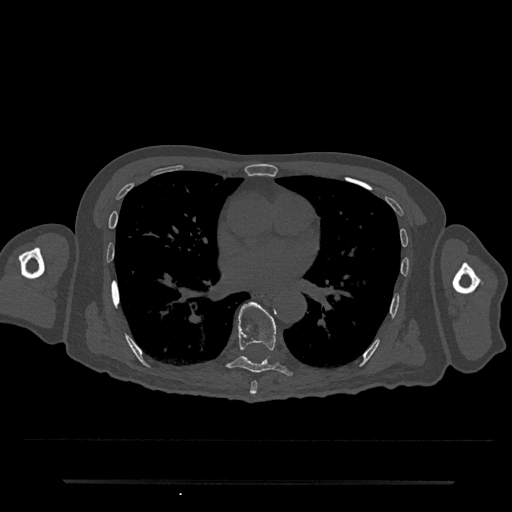
CT including the spine, one axial slice; position 427 of 797 along the scan axis; 120 kVp; bone window (W 1800 / L 400 HU); 0.5 mm slice thickness; 512 × 512 image matrix, field of view 427 × 427 mm. Patient: male, 74 years. From the clinical record (not read from this slice): primary cancer: prostate.
Structures marked on this image (semi-automatically segmented with operator editing):
- T7 vertebra: bounding box <250,381,258,395> (left, top, right, bottom; pixels)
- T8 vertebra: <227,302,292,376>